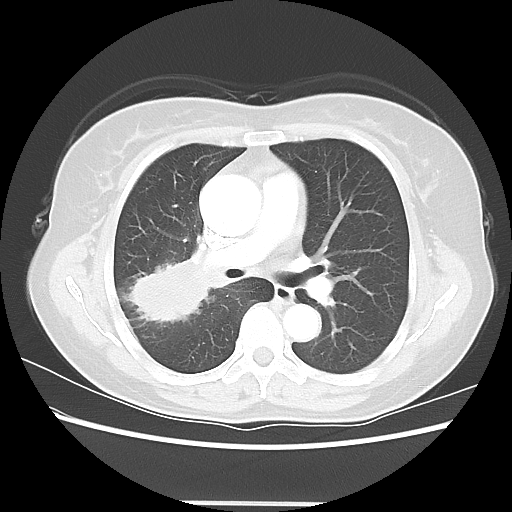
Chest CT, one axial slice; slice 35 of 56 in the series (ordered by position); 120 kVp; lung window (W 1500 / L -600 HU); 512 × 512 image matrix, field of view 360 × 360 mm. Patient: female, 55 years. From the clinical record (not read from this slice): clinical TNM (as recorded): T2 N1 M0.
Outlined on this slice (rectangle marked by the reading radiologist):
- lung tumour (recorded histology: adenocarcinoma): bounding box (x1, y1, x2, y2) in pixels: (121, 258, 222, 333)